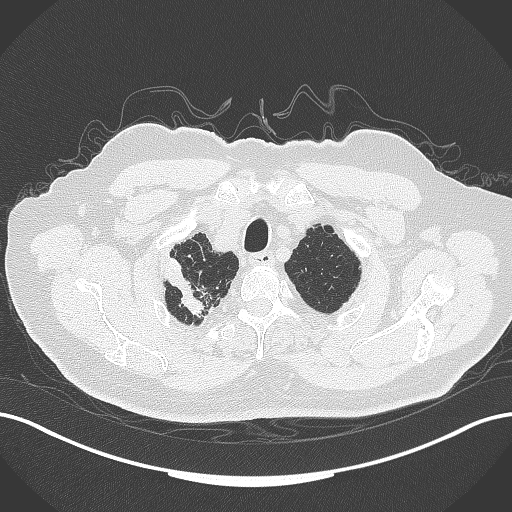
Chest CT, one axial slice. Position 324 of 389 along the scan axis. 120 kVp. Lung window (W 1500 / L -600 HU). 1 mm slice thickness. 512 × 512 image matrix. Patient: male, 72 years. From the clinical record (not read from this slice): clinical TNM (as recorded): T1a N0 M0.
Annotated regions visible in this slice (rectangle marked by the reading radiologist):
- lung tumour (recorded histology: squamous cell carcinoma): box from (x=165, y=252) to (x=205, y=315) px